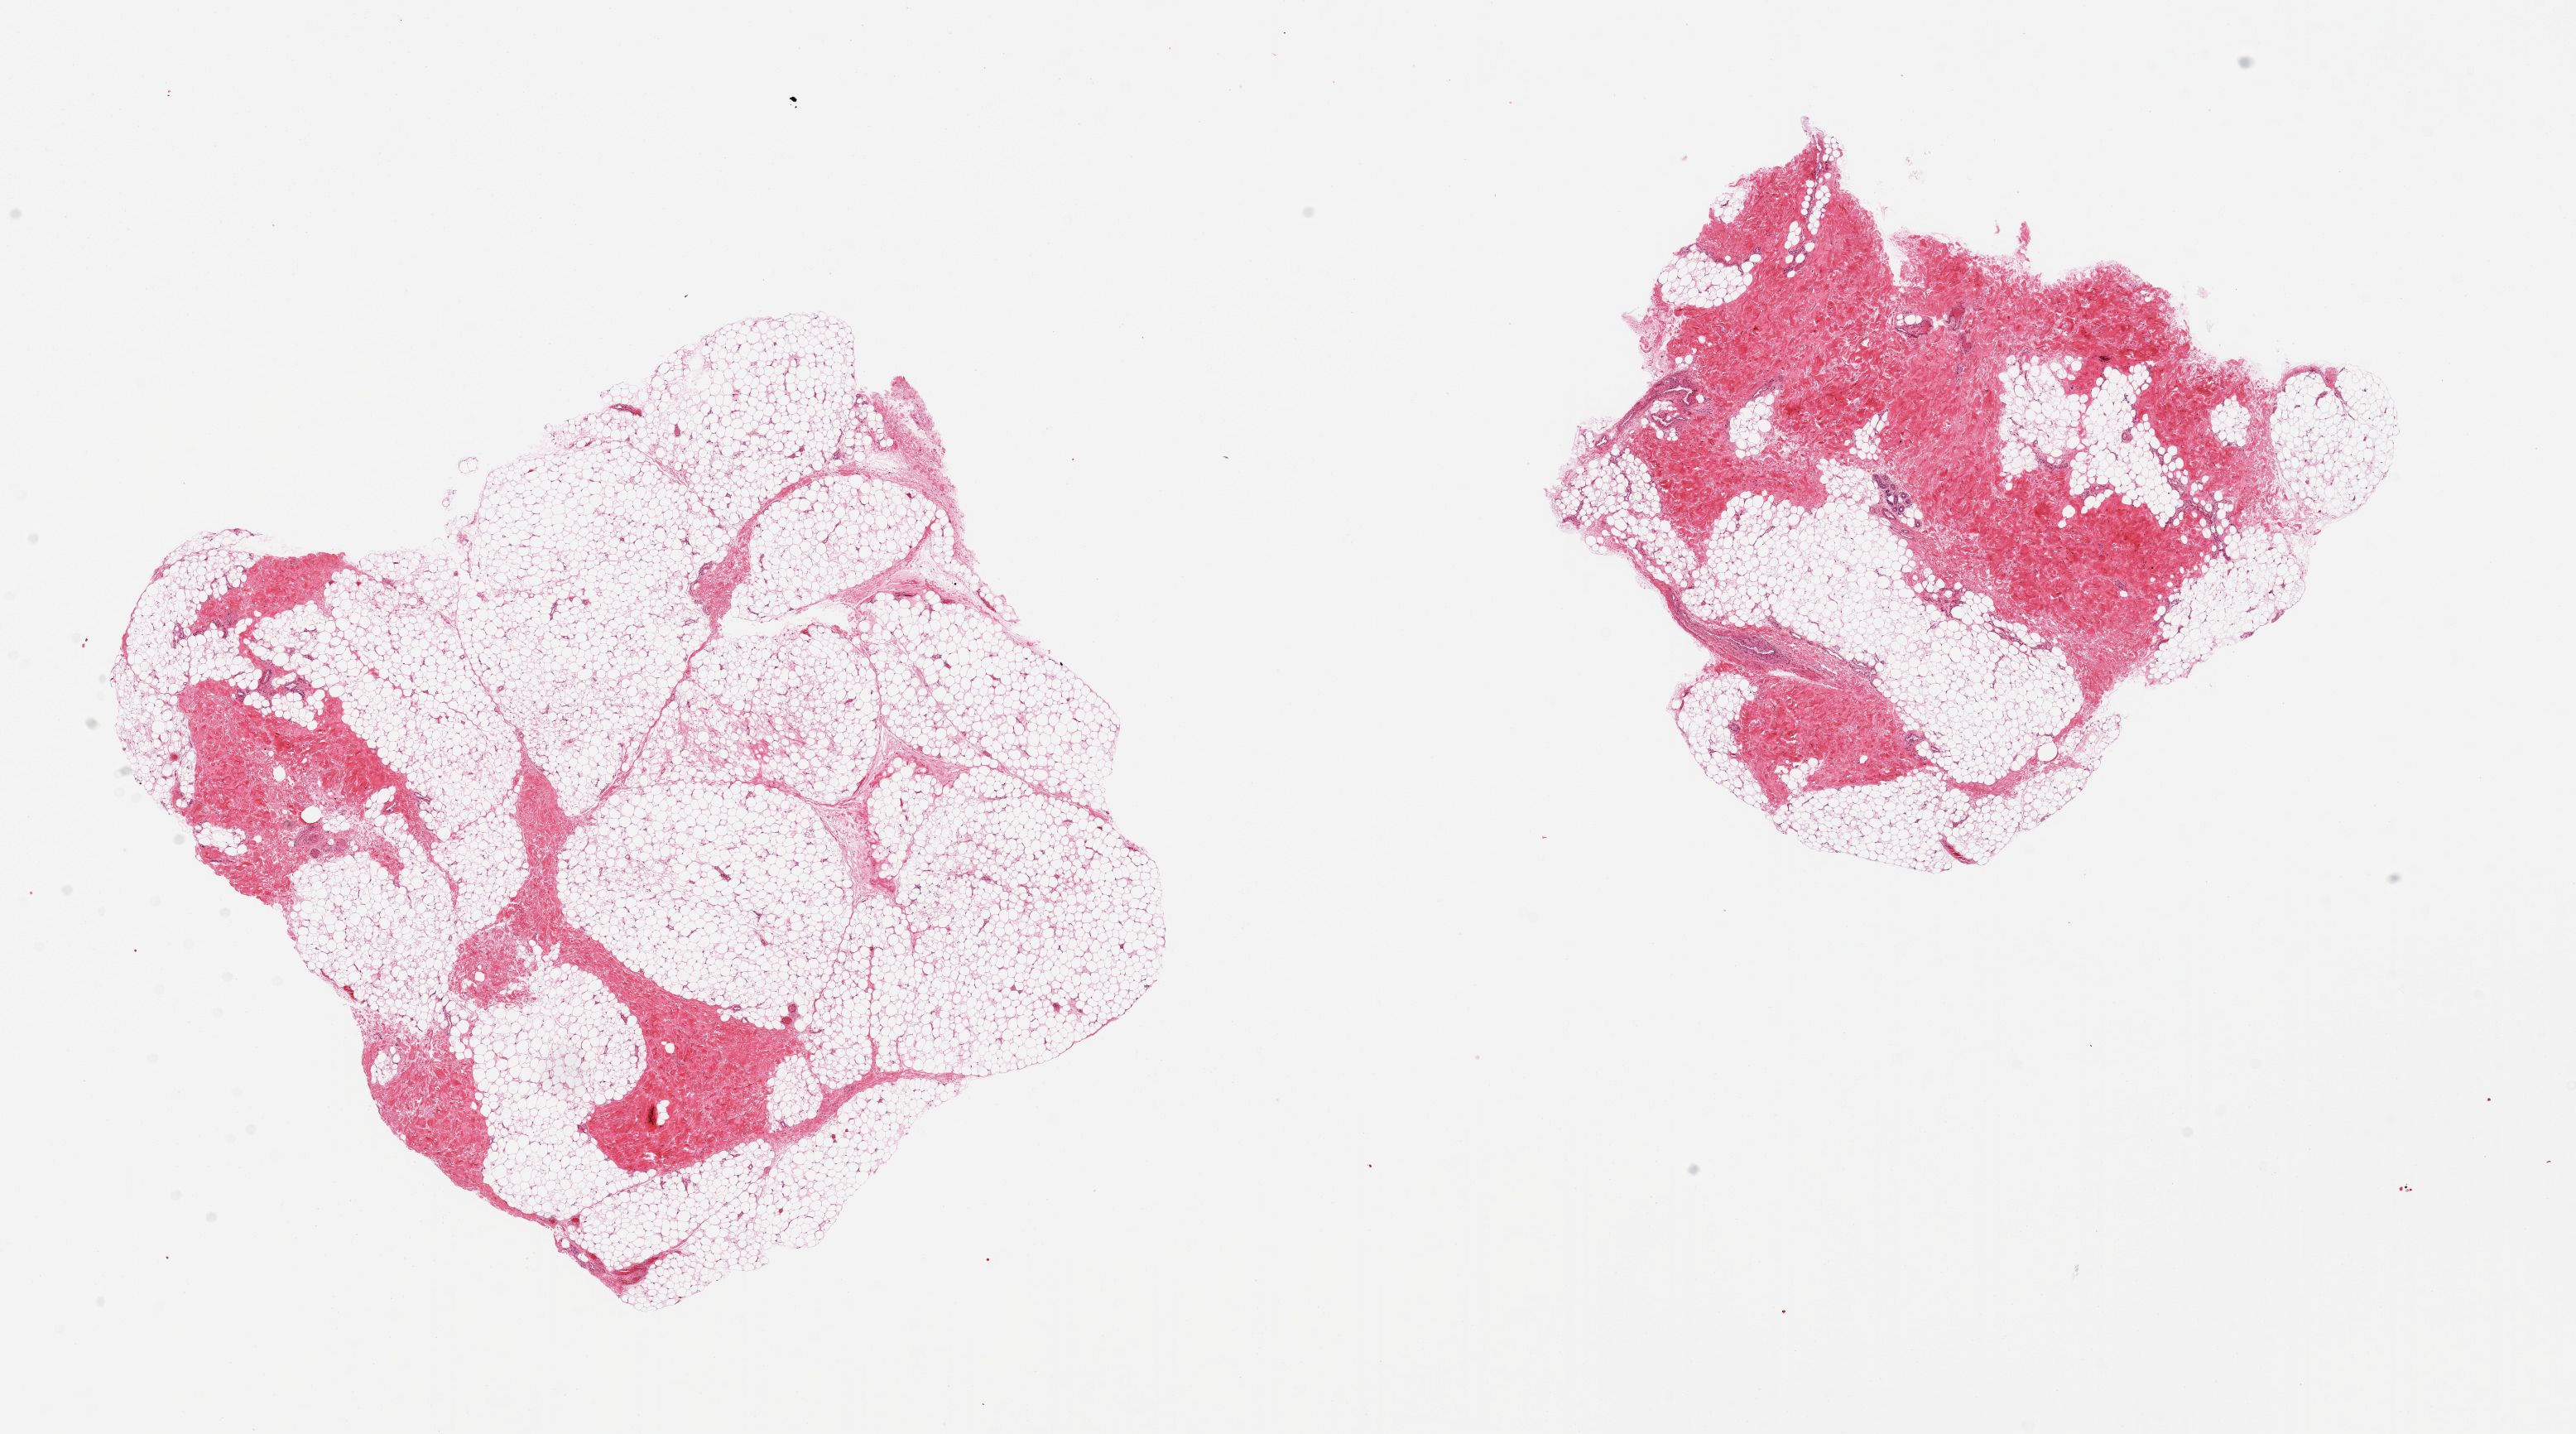
Hematoxylin and eosin (H&E) whole-slide image, whole scanned area (about 24.6 x 13.7 mm, slide scanned at 20x) shown as a low-resolution overview. PAXgene-fixed paraffin-embedded (PFPE) section. Section of adipose tissue (target tissue). Donor tissue sample. Donor sex: male.
Reviewer comment on this tissue sample: 2 pieces; 1 piece is 60% fibrous, also contains a sweat gland; other has 10% fibrous tissue.